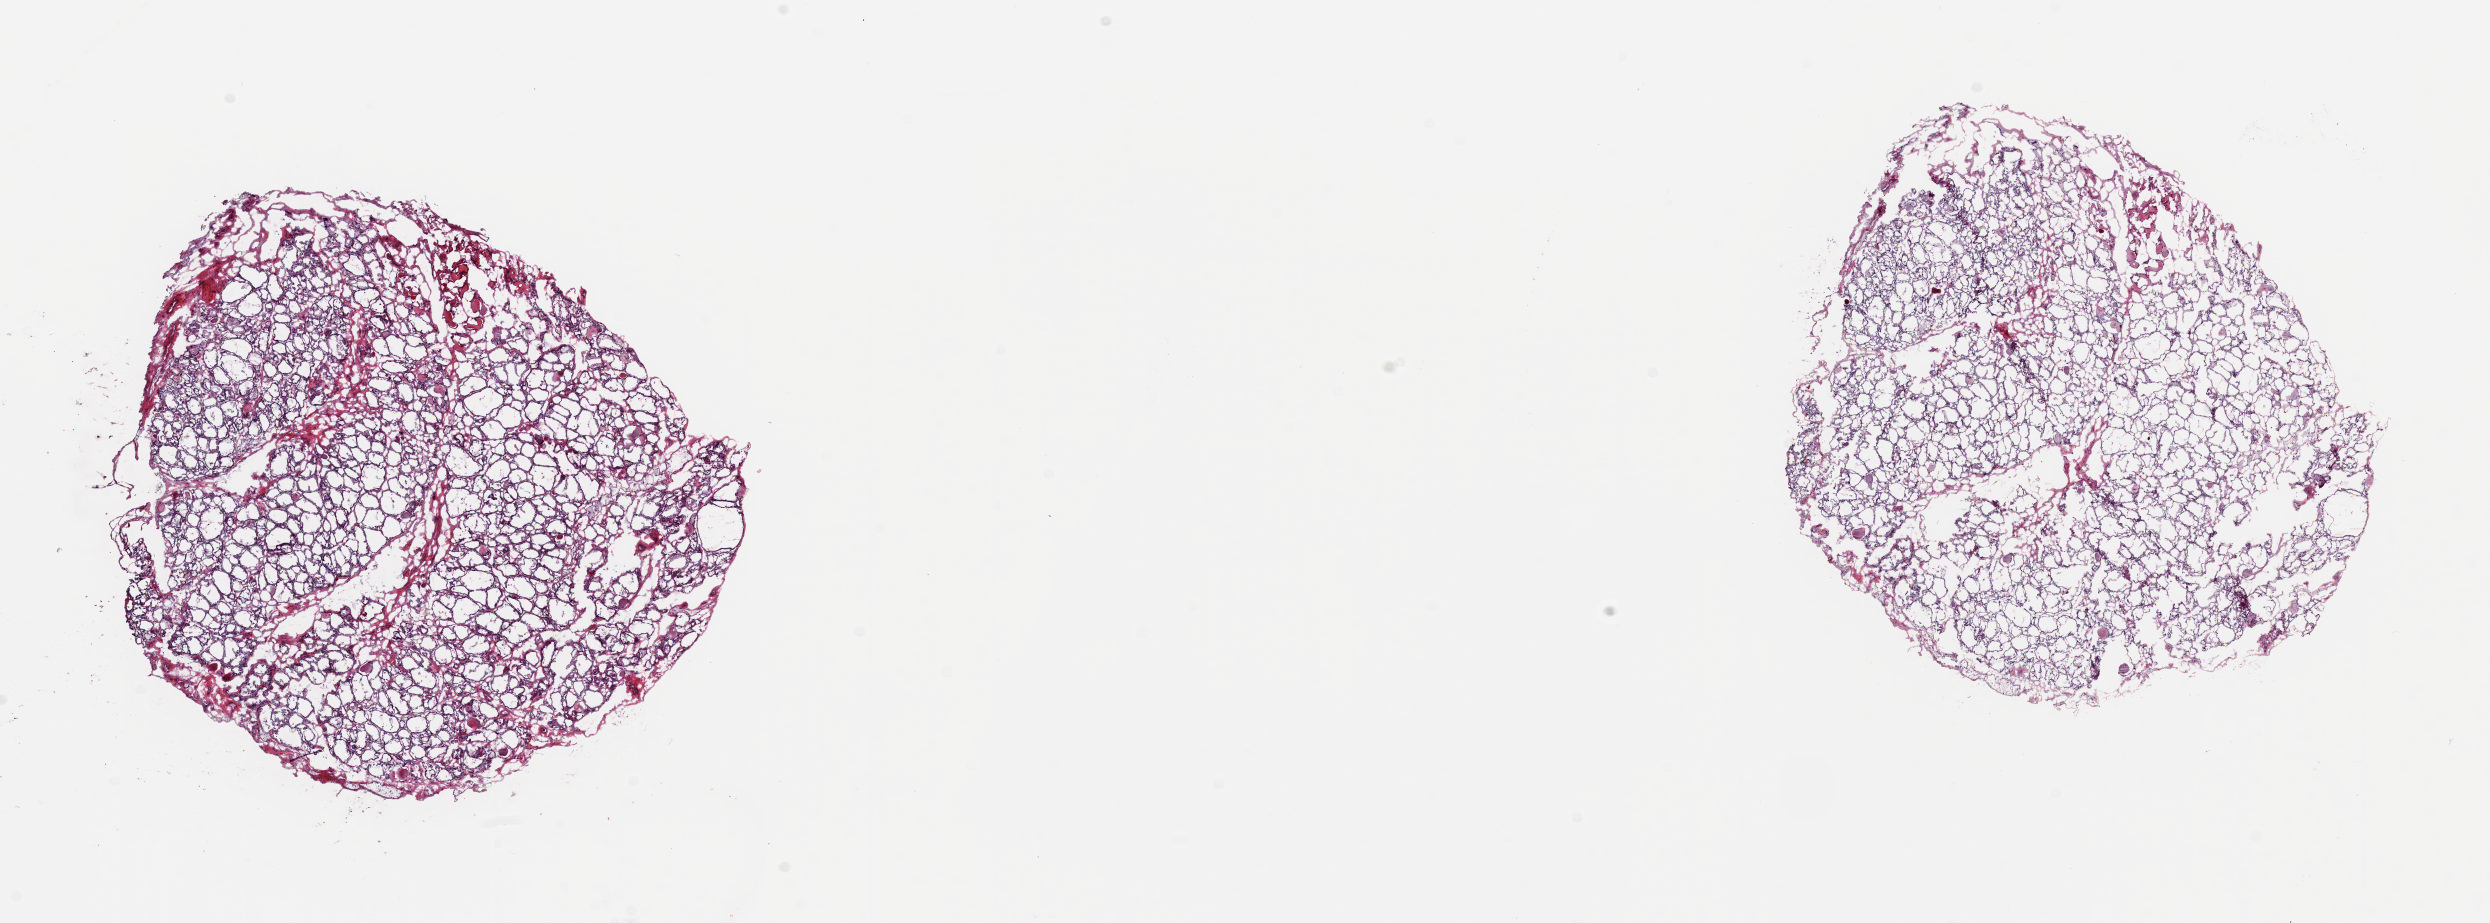
Whole-slide histology image, Hematoxylin and eosin (H&E) stained, shown as a low-resolution overview of the whole scanned area (about 19.7 x 7.3 mm), frozen section from the top of the tissue portion, thyroid, solid tissue normal (non-tumour tissue) sample. Patient: female, age at initial diagnosis 66 years.
This section: solid tissue normal sample (biorepository sample class). Patient diagnosis: Papillary adenocarcinoma, NOS (thyroid gland).